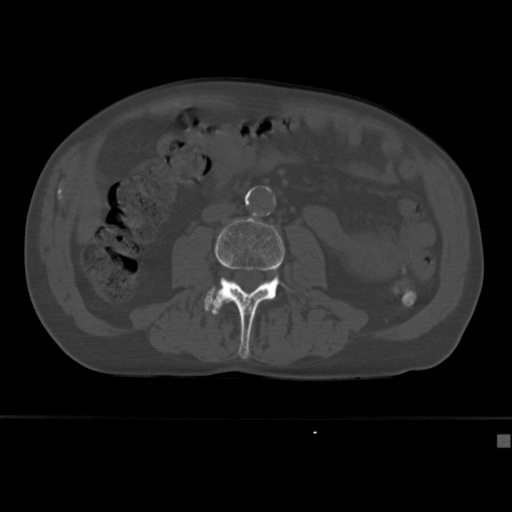
CT including the spine, one axial slice. Slice 125 of 430 in the series (ordered by position). Bone window (W 1800 / L 400 HU). 1.5 mm slice thickness. 512 × 512 image matrix, field of view 337 × 337 mm. Male patient, age 64 years. Case-level facts recorded for this patient, not image findings: primary cancer: uterus.
Annotated regions visible in this slice (semi-automatic segmentation, software-assisted and operator-edited):
- L3 vertebra: bounding box (x1, y1, x2, y2) in pixels: (210, 217, 293, 359)
- L4 vertebra: (204, 288, 215, 312)